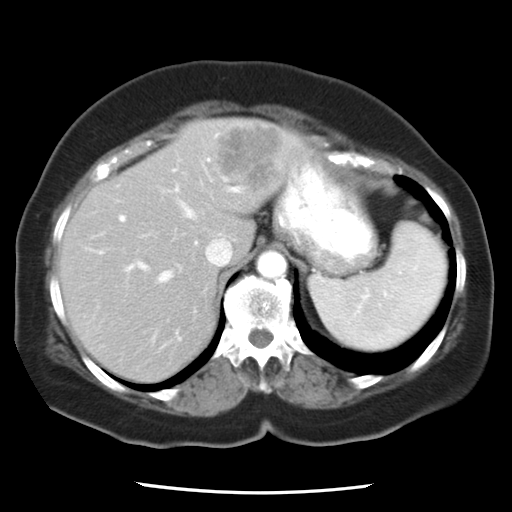
Contrast-enhanced abdominal CT, one axial slice. Position 18 of 24 along the scan axis. 120 kVp. Soft-tissue window (W 400 / L 40 HU). 7.5 mm slice thickness. 512 × 512 image matrix. Female patient, age 71 years. Case-level facts recorded for this patient, not image findings: diagnosis: colorectal cancer liver metastases, imaged before liver resection; multiple liver metastases: no; largest metastasis: 4.3 cm; disease in both lobes: no.
Structures marked on this image (manually delineated by an expert):
- hepatic veins: bounding box [x1, y1, x2, y2] px = [137, 178, 235, 284]
- liver: [60, 119, 309, 381]
- planned liver remnant (the part of the liver to remain after resection): [61, 137, 250, 381]
- portal vein (with intrahepatic branches): [120, 135, 245, 339]
- liver metastasis: [208, 122, 289, 194]